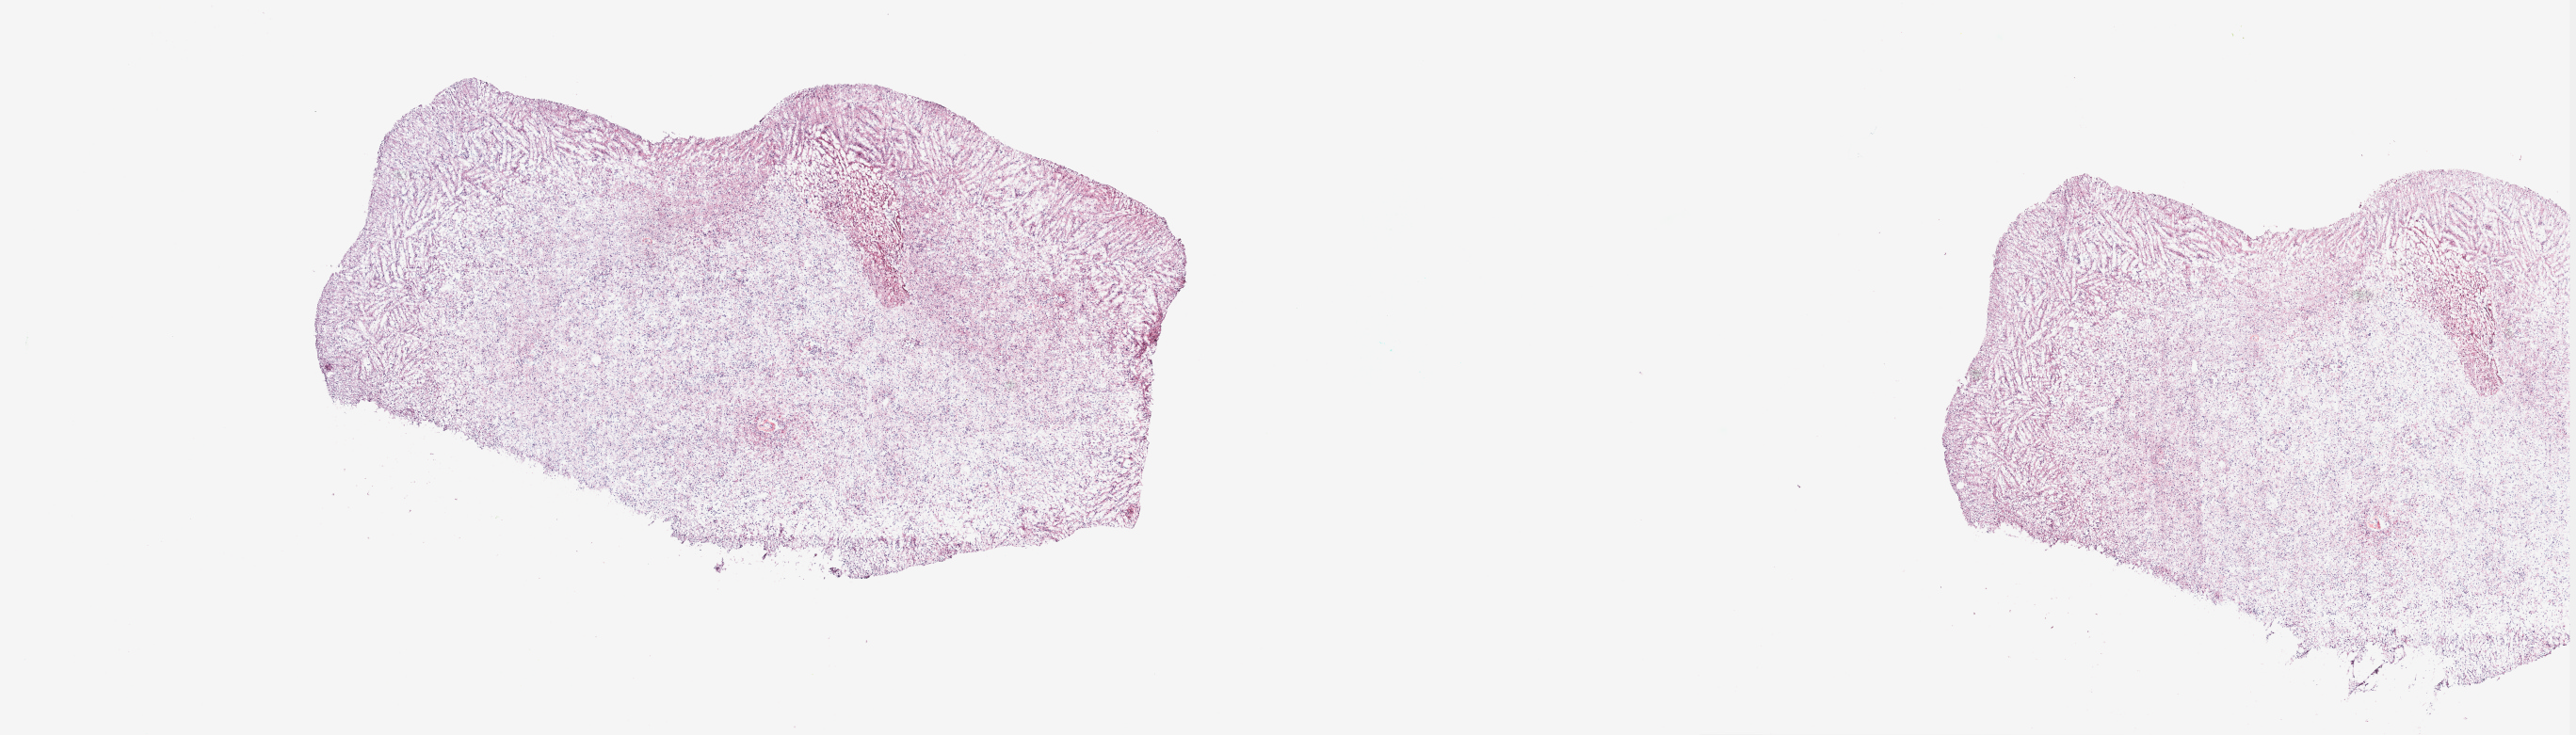
H&E-stained whole-slide image — shown as a low-resolution overview of the whole scanned area (about 21.7 x 6.2 mm, acquisition: 40x scan), frozen section from the top of the tissue portion, sample: primary tumour, brain. Female, age 44 years at initial diagnosis. Histologic grade: G3 (poorly differentiated). Slide review estimates, as recorded: tumour cells 60%, tumour nuclei 90%, normal cells 5%, stromal cells 35%, necrosis 0%. Inflammatory infiltration, as recorded: lymphocyte infiltration 0%, monocyte infiltration 0%, neutrophil infiltration 0%.
- pathologic diagnosis: Astrocytoma, anaplastic (cerebrum)